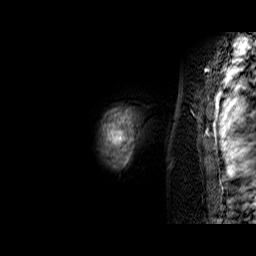
Breast MRI (dynamic contrast-enhanced), one sagittal slice. Slice 58 of 60 in the series (ordered by position). Dynamic contrast-enhanced series, time point 2 of 6 at this slice position (early post-contrast). 1.5 T. TE 6.4 ms, TR 32.9 ms. 256 × 256 image matrix, field of view 200 × 200 mm. Female patient. Case-level facts recorded for this patient, not image findings: setting: breast cancer imaged before/during neoadjuvant chemotherapy; receptor status: triple-negative.
Annotated regions visible in this slice (semi-automatic segmentation, software-assisted and operator-edited):
- analysis volume of interest (the breast-tissue region the enhancement analysis was run in; not a lesion): bounding box (x1, y1, x2, y2) in pixels: (103, 109, 139, 168)
- tumour enhancement mask (voxels above the 100 % enhancement threshold inside the analysis volume of interest): (103, 109, 134, 167)